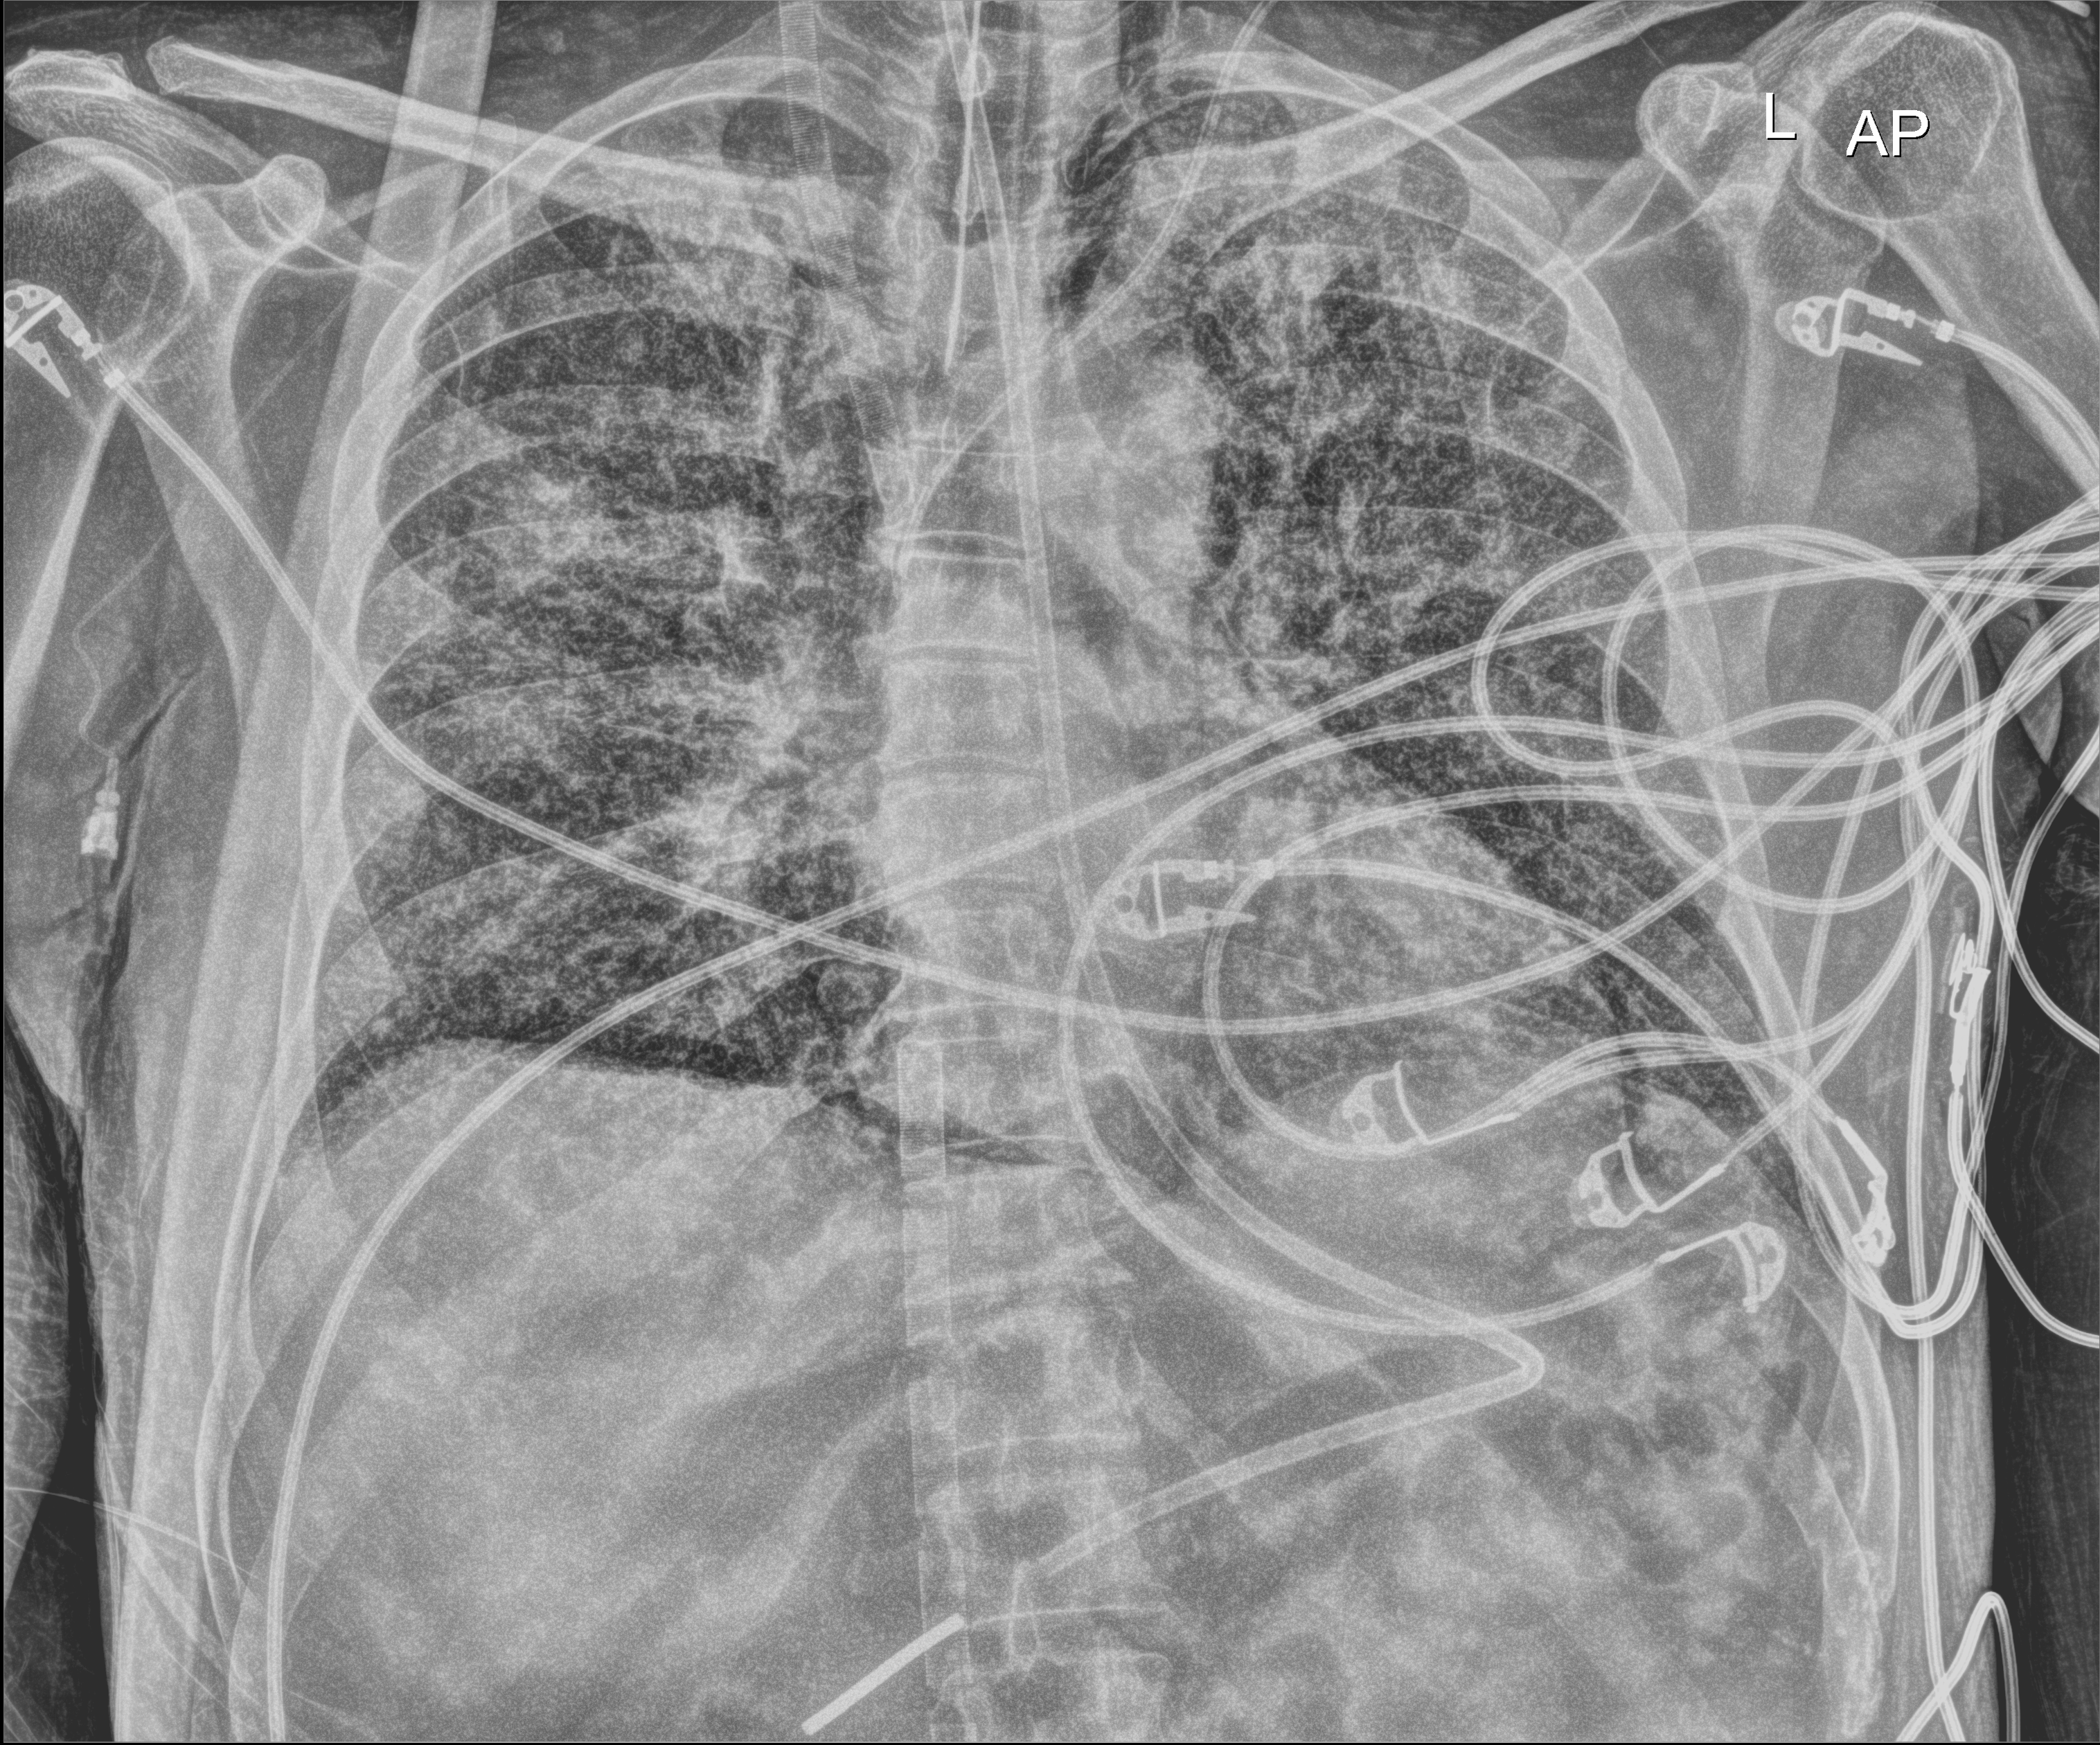
Chest X-ray; anteroposterior (AP) projection. Patient hospitalised with COVID-19; male, aged 18–59 years.
Hospital-stay facts (about this admission, not read from this image; timing relative to this image not recorded): diabetes (admission record): no; mechanically ventilated during this hospital stay: yes; admitted to intensive care during this hospital stay: yes.